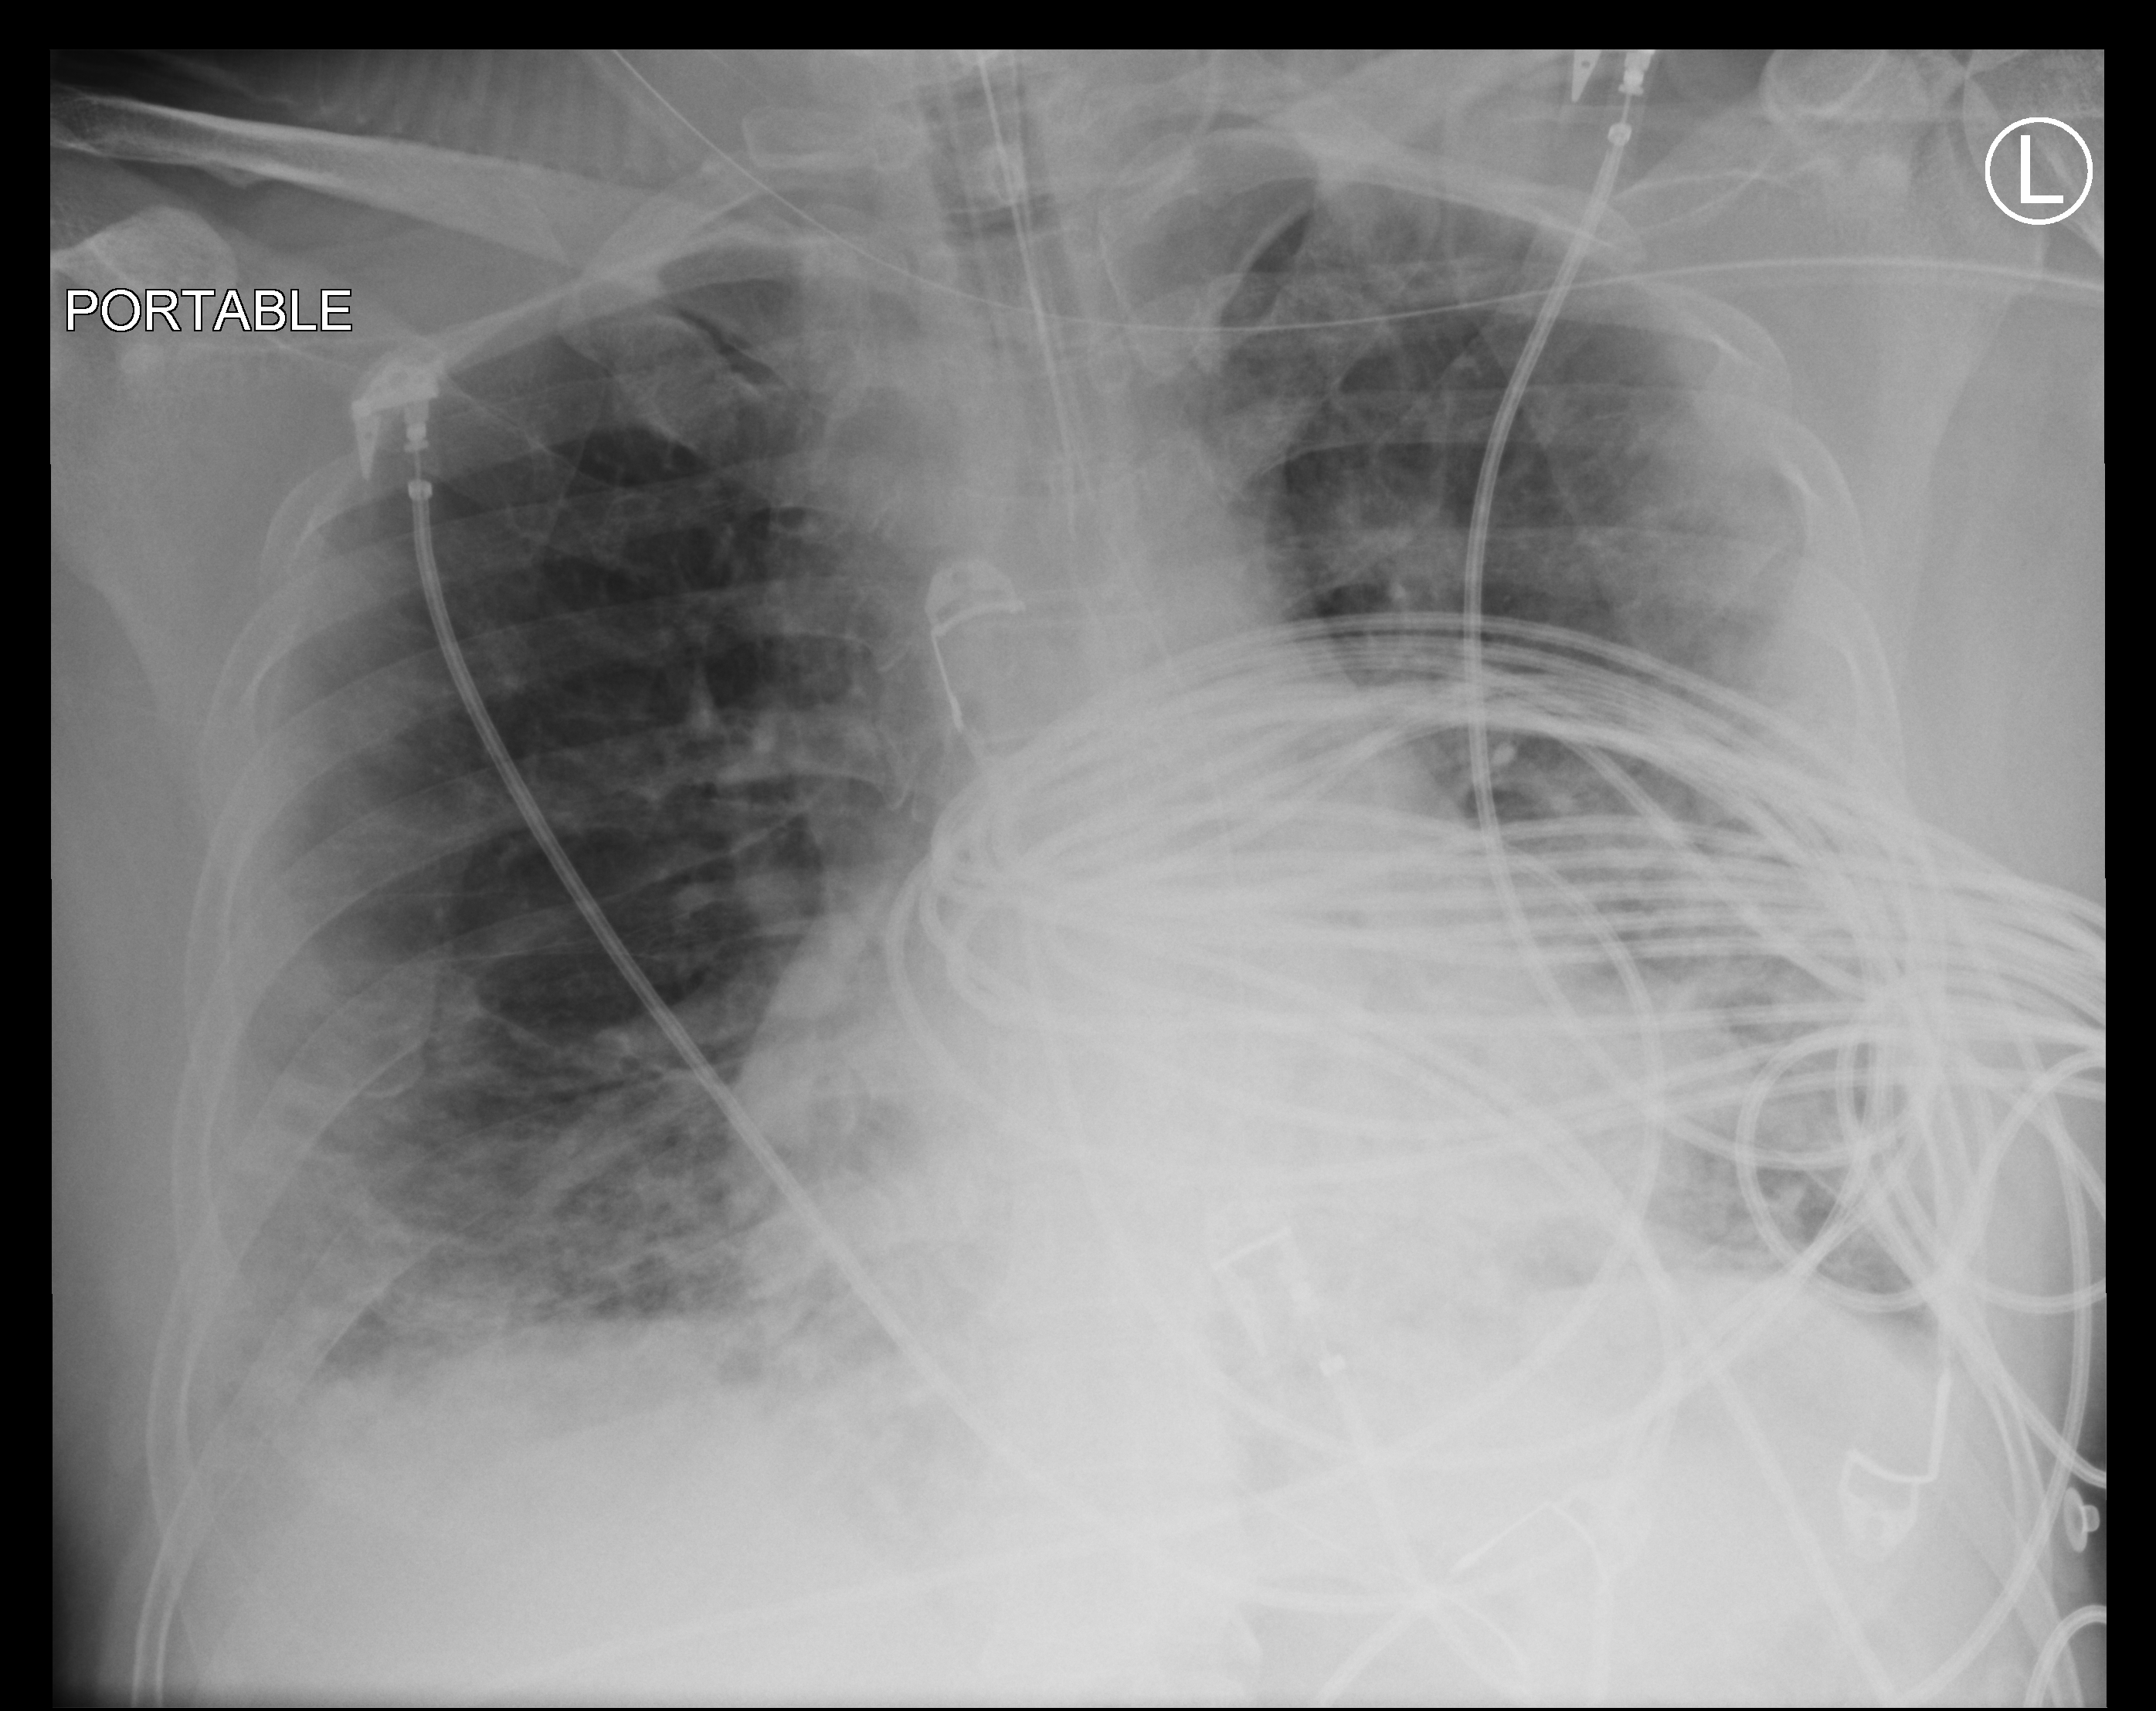
Chest X-ray (portable); anteroposterior (AP) projection. Male patient hospitalised with COVID-19, age 18–59 years.
Hospital-stay facts (about this admission, not read from this image; timing relative to this image not recorded): mechanically ventilated during this hospital stay: yes; smoking status (admission record): former.